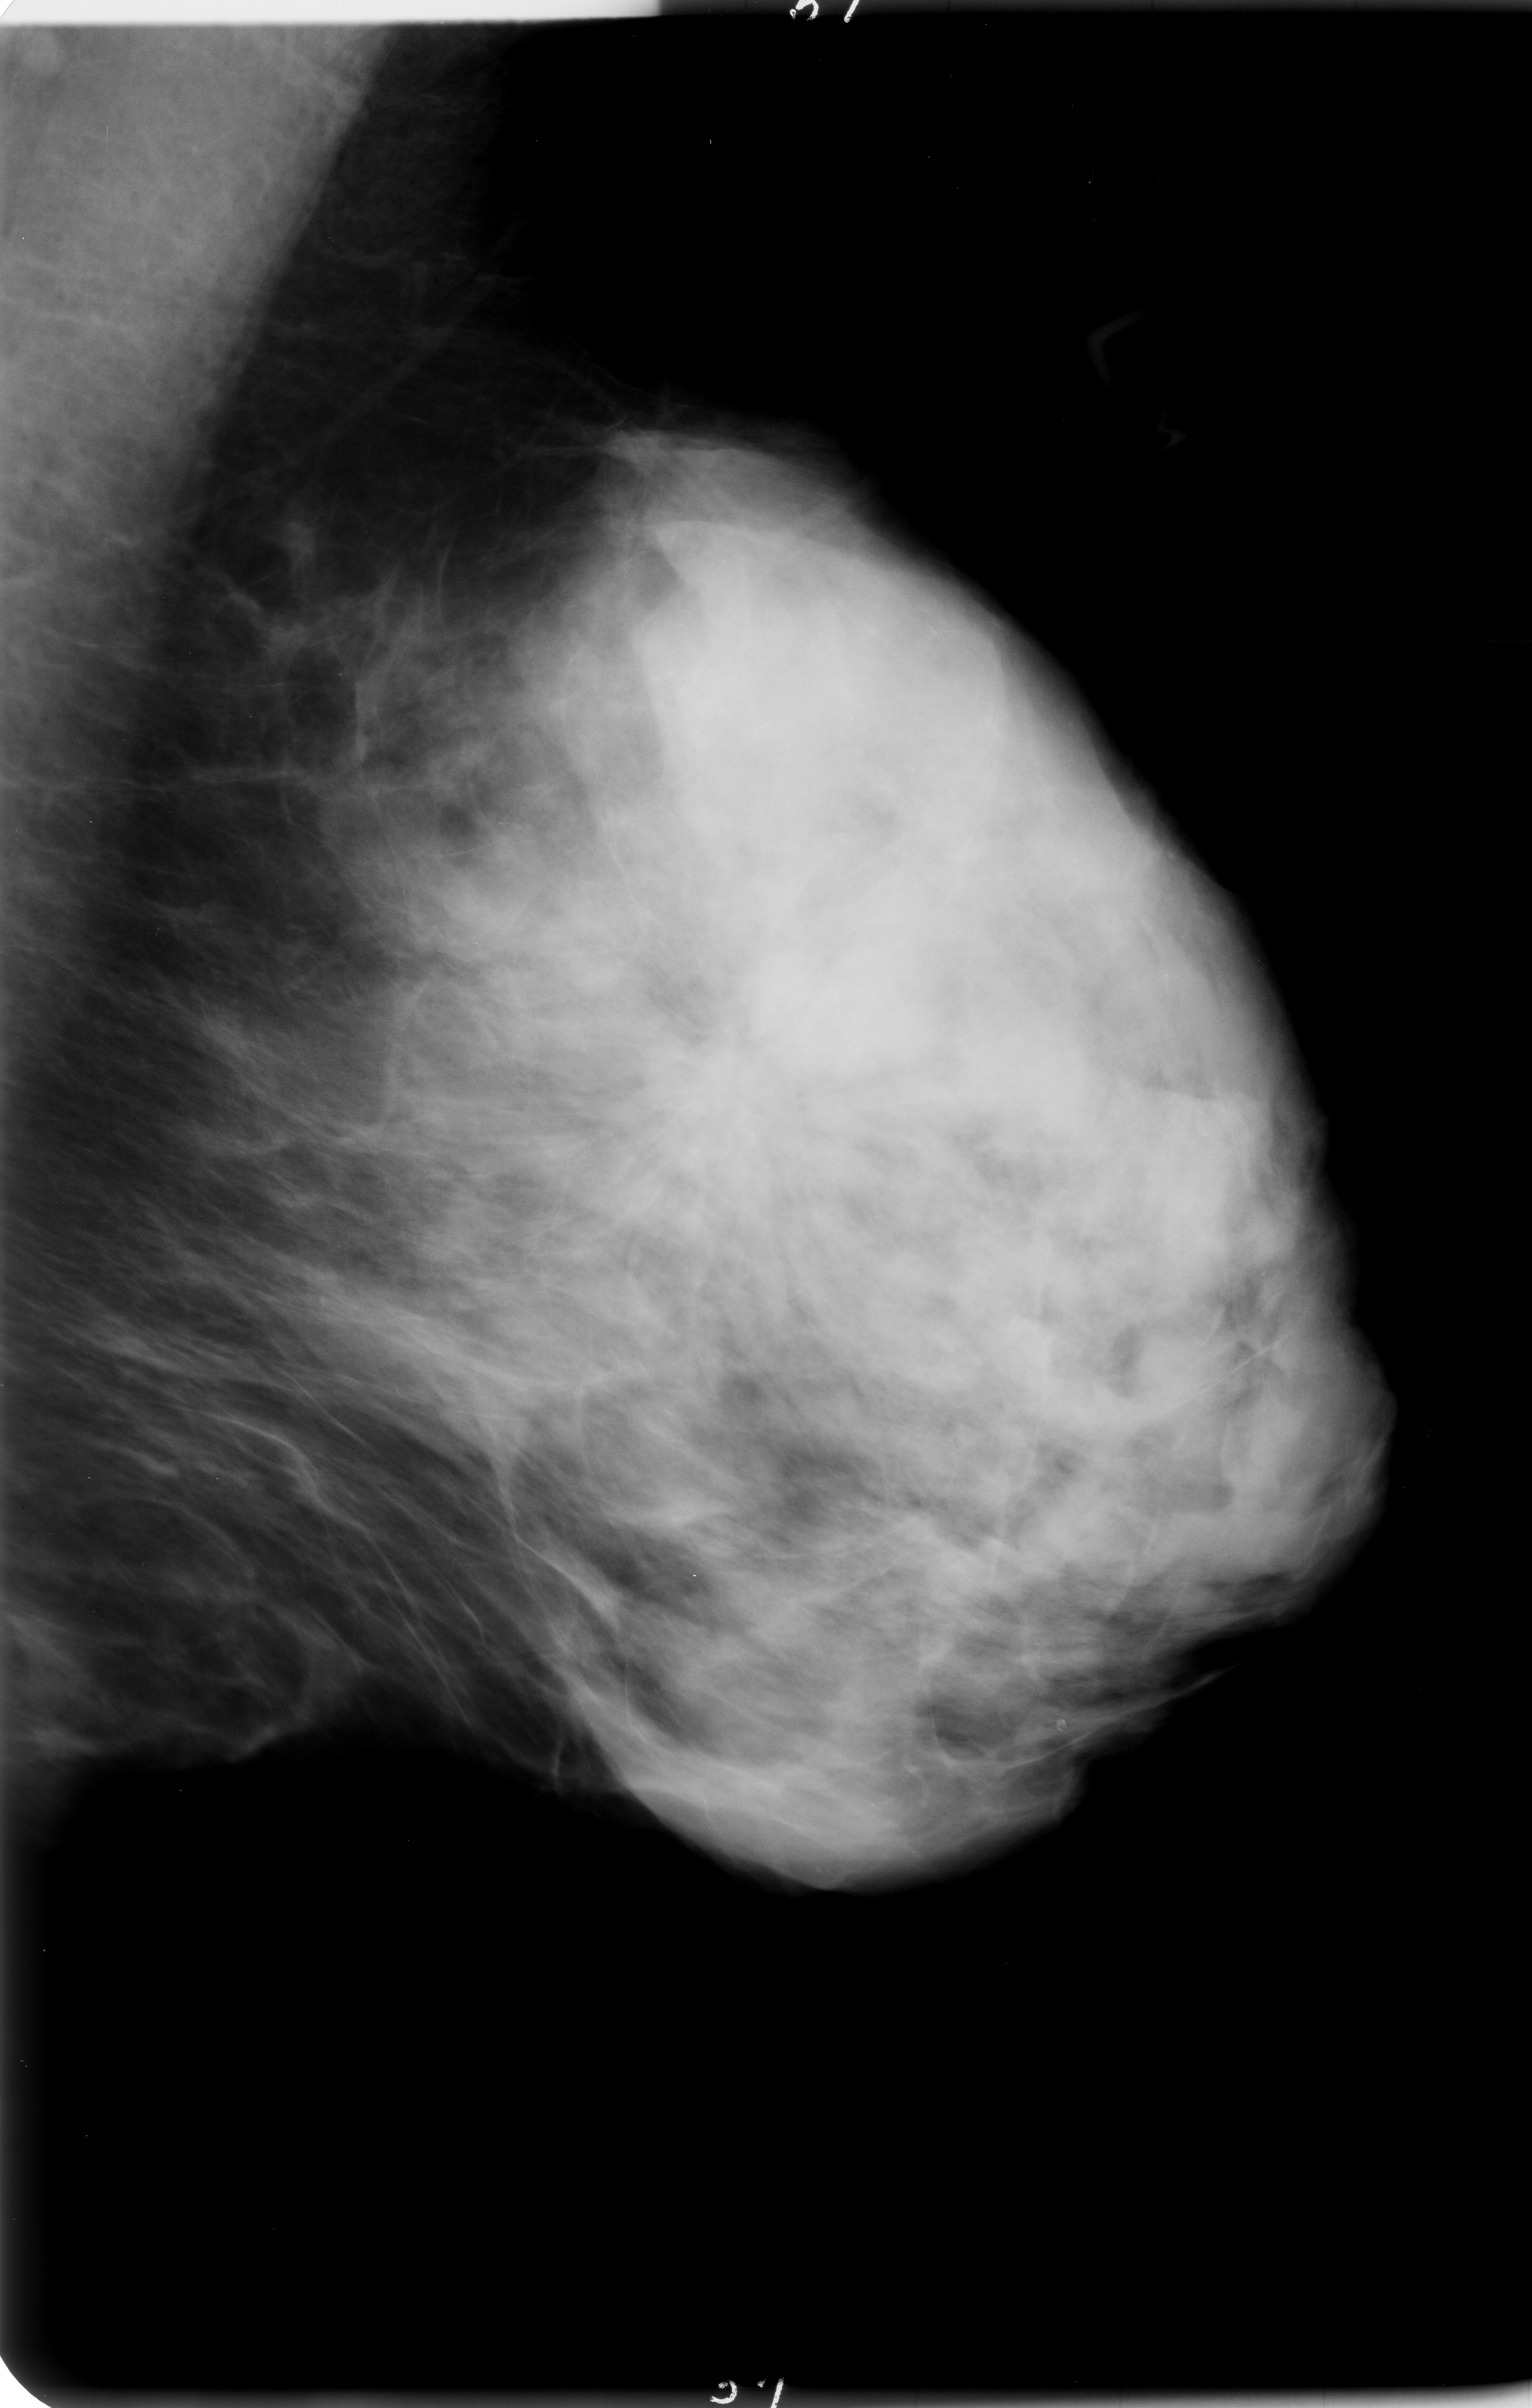
Mammogram (digitized film). Left breast. MLO view. Breast composition: extremely dense (BI-RADS density category 4 of 4). 1532 × 2408 image matrix.
Expert-marked regions of interest on this image (one box per marked abnormality):
- calcifications, morphology pleomorphic, distribution clustered; BI-RADS assessment category 5; subtlety rating 3 on a 1 (subtle) to 5 (obvious) scale; pathology result (as recorded, not read from the image): malignant: box from (x=499, y=863) to (x=1072, y=1322) px